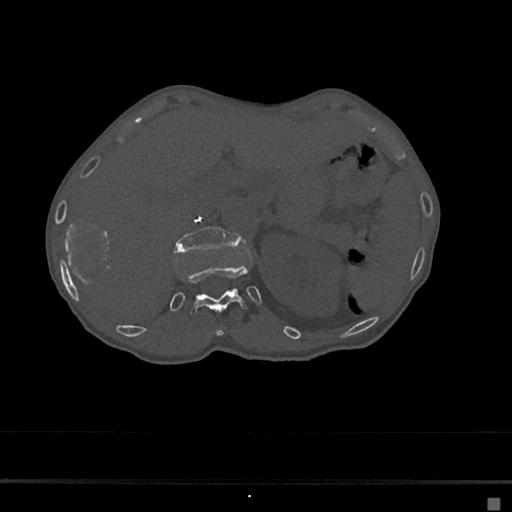
CT including the spine, one axial slice. Slice 117 of 797 in the series (ordered by position). 120 kVp. Bone window (W 1800 / L 400 HU). 0.5 mm slice thickness. 512 × 512 image matrix, field of view 360 × 360 mm. Female patient, age 68 years. From the clinical record (not read from this slice): primary cancer: renal.
Annotated regions visible in this slice (semi-automatically segmented with operator editing):
- L1 vertebra: bounding box (x1, y1, x2, y2) in pixels: (173, 226, 240, 254)
- T11 vertebra: (216, 329, 224, 337)
- T12 vertebra: (181, 264, 248, 316)